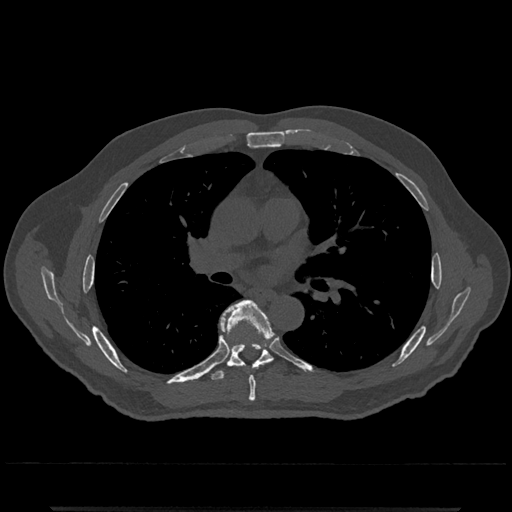
CT including the spine, one axial slice. Position 747 of 797 along the scan axis. Reconstruction kernel Br40s/3. Bone window (W 1800 / L 400 HU). 0.5 mm slice thickness. 512 × 512 image matrix, field of view 393 × 393 mm. Patient: male, 67 years. From the clinical record (not read from this slice): primary cancer: prostate.
Annotated regions visible in this slice (semi-automatically segmented with operator editing):
- T6 vertebra: bounding box [x1, y1, x2, y2] px = [225, 300, 273, 402]
- T7 vertebra: [209, 320, 273, 382]